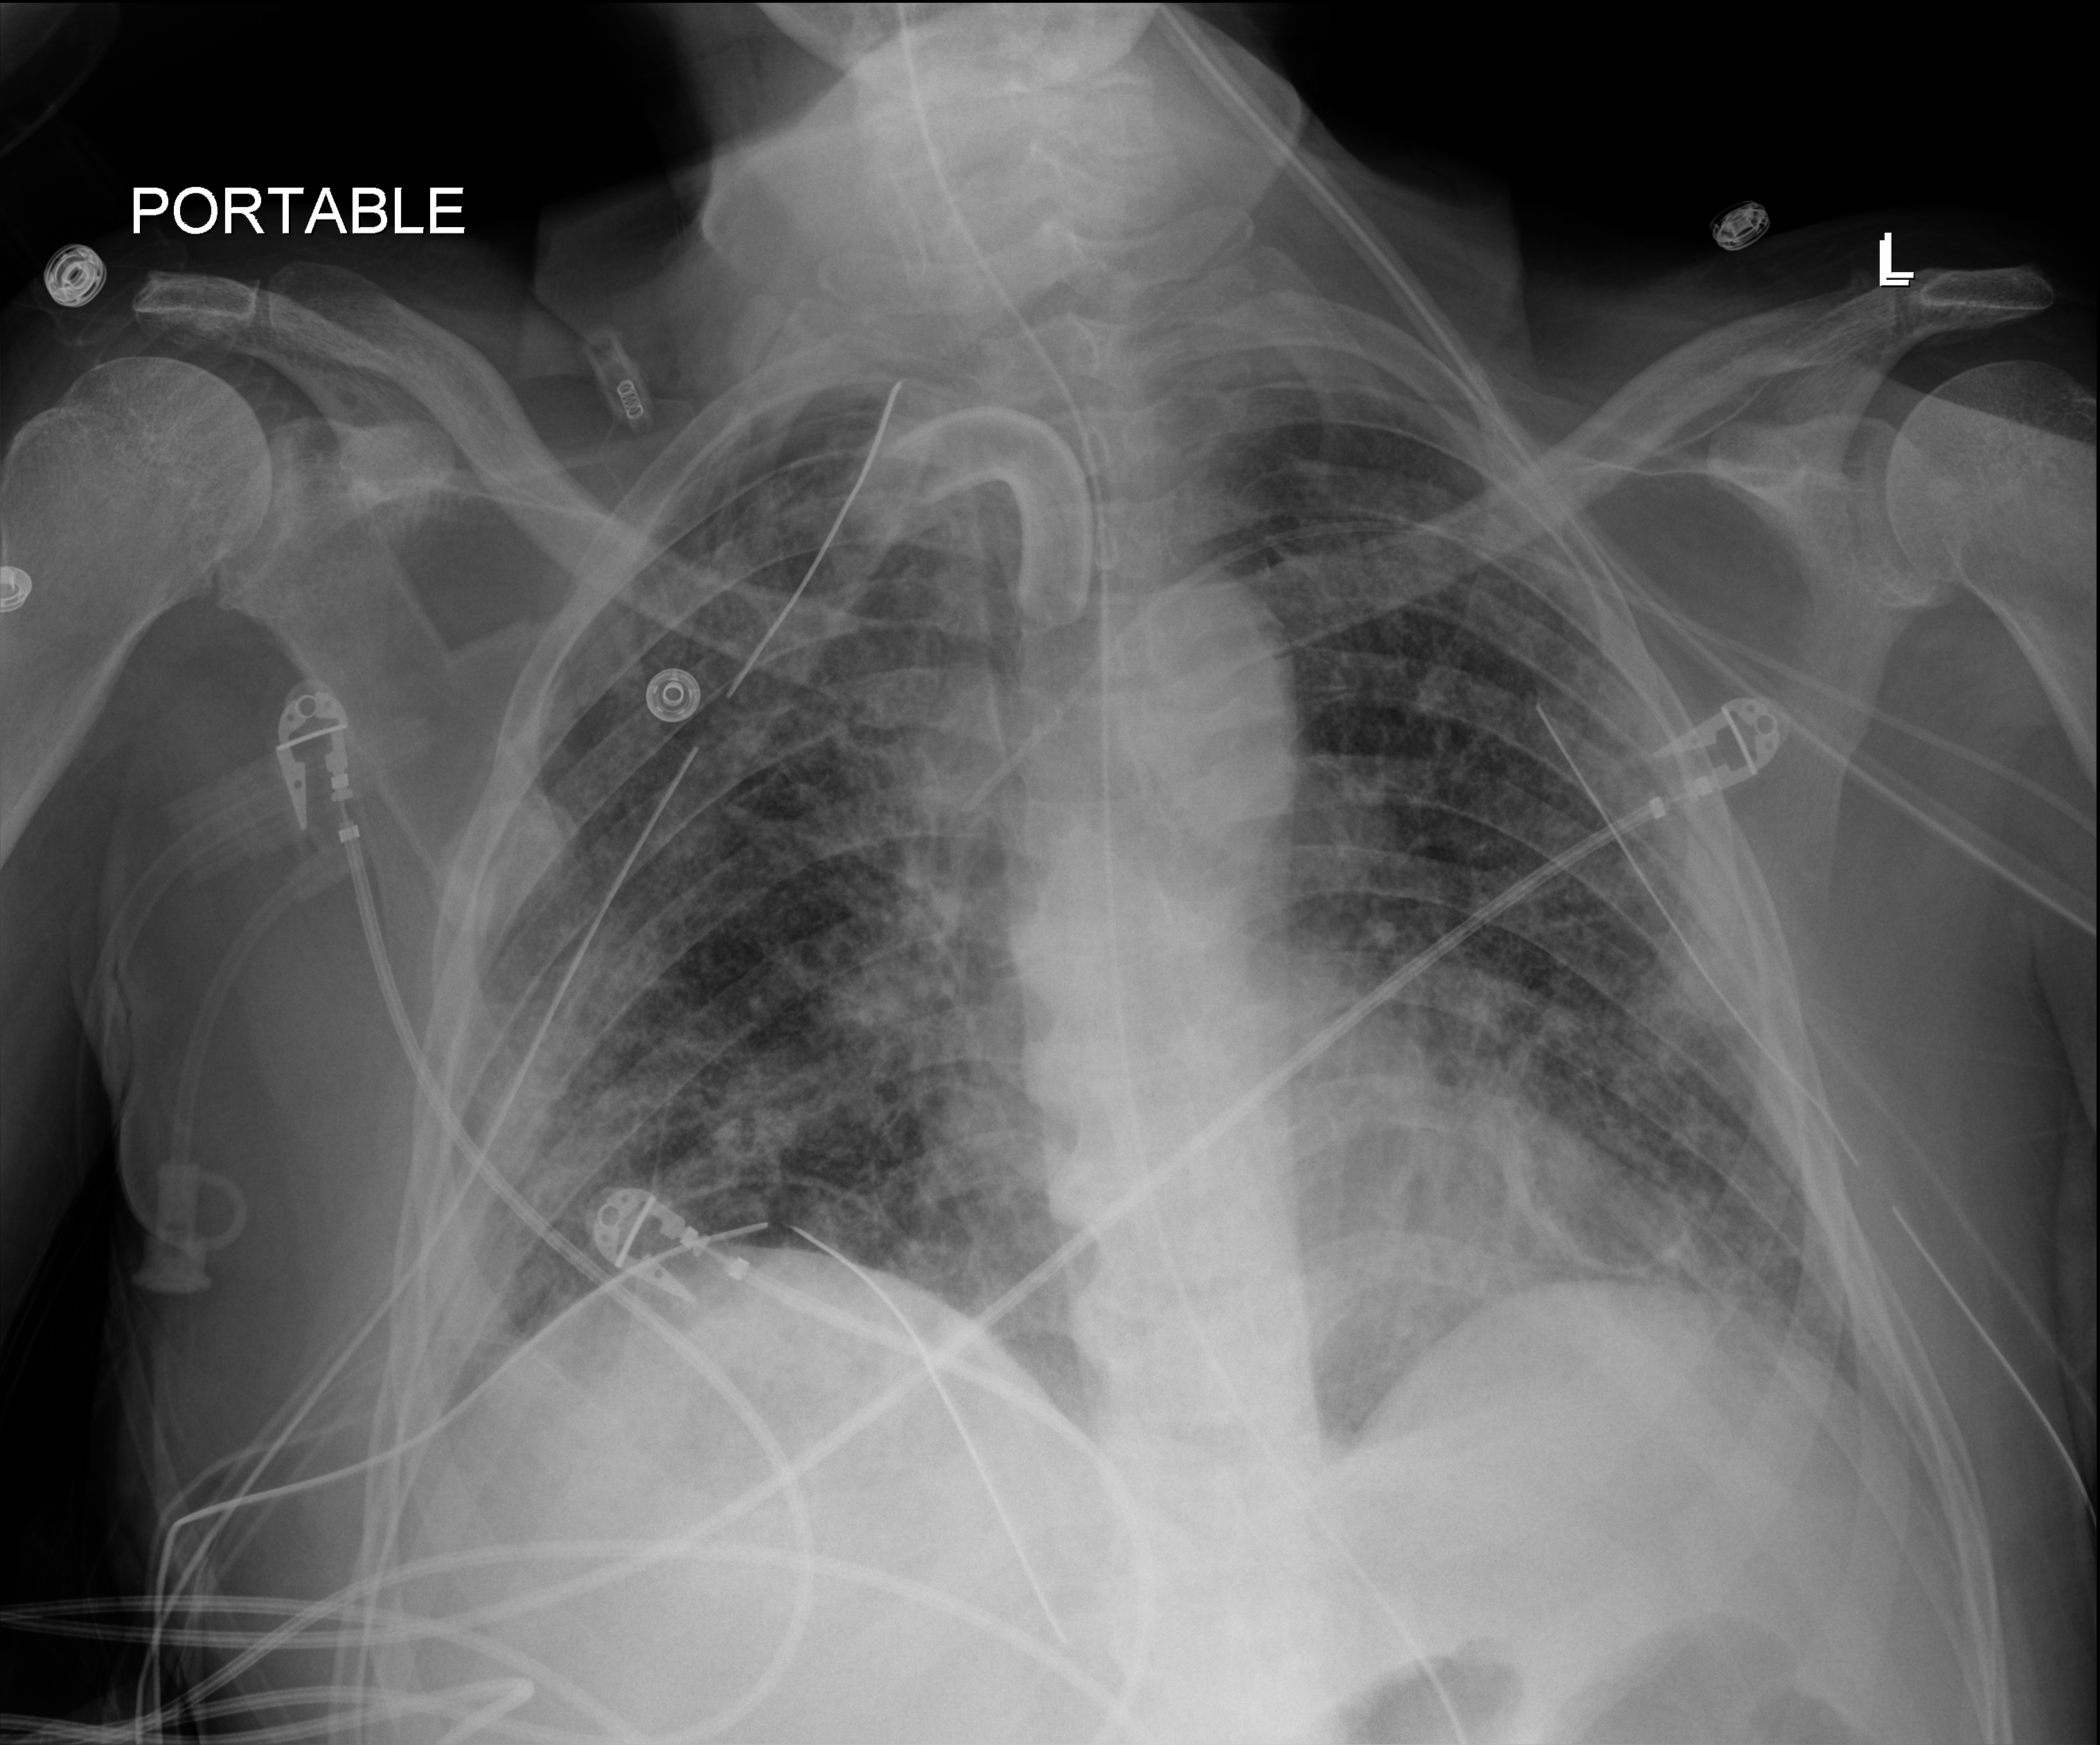
Portable chest radiograph; anteroposterior (AP) projection. Patient hospitalised with COVID-19; male, aged 18–59 years.
From the hospital-stay record, not from the radiograph (when in the stay this image was taken is not recorded): COPD (admission record): no.